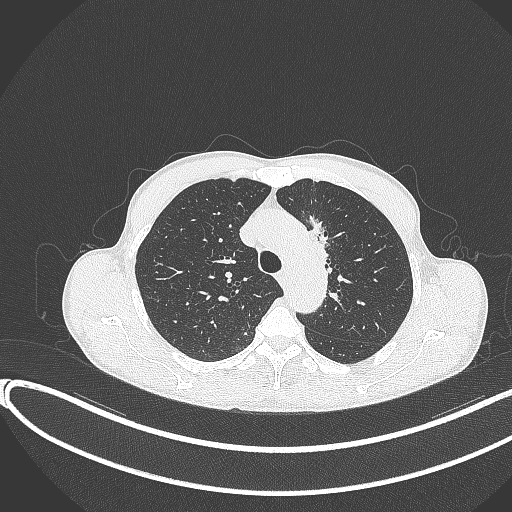
Chest CT, one axial slice. Slice 280 of 374 in the series (ordered by position). Reconstruction kernel B70f. 120 kVp. Lung window (W 1500 / L -600 HU). 1 mm slice thickness. 512 × 512 image matrix, field of view 400 × 400 mm. Patient: male, 58 years. Case-level facts recorded for this patient, not image findings: clinical TNM (as recorded): T1c N1 M0.
Structures marked on this image (bounding box drawn by a radiologist):
- lung tumour (recorded histology: adenocarcinoma): box from (x=304, y=207) to (x=339, y=268) px